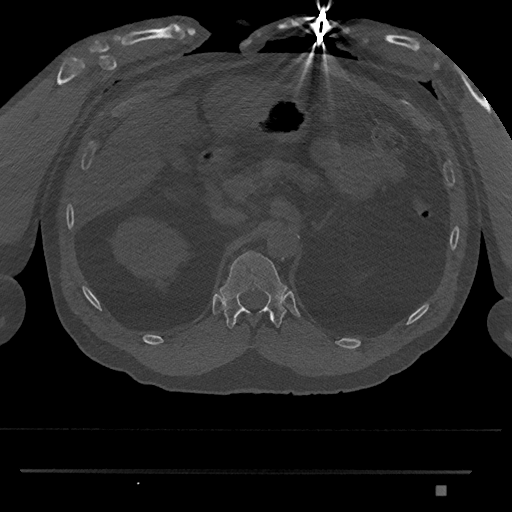
CT including the spine, one axial slice. 120 kVp. Bone window (W 1800 / L 400 HU). 0.5 mm slice thickness. 512 × 512 image matrix, field of view 429 × 429 mm. Male patient, age 65 years. Case-level facts recorded for this patient, not image findings: primary cancer: prostate.
Outlined on this slice (semi-automatically segmented with operator editing):
- T12 vertebra: box from (x=219, y=250) to (x=287, y=329) px